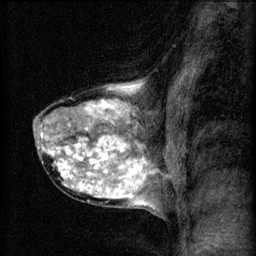
Breast MRI (dynamic contrast-enhanced), one sagittal slice. Position 36 of 60 along the scan axis. 3 images stored at this slice position (order not interpretable as contrast timing). 1.5 T. TE 4.2 ms, TR 8.2 ms. 2 mm slice thickness. 256 × 256 image matrix. Female patient, age 40 years.
Outlined on this slice (semi-automatic segmentation, software-assisted and operator-edited):
- analysis volume of interest (the breast-tissue region the enhancement analysis was run in; not a lesion): bounding box <33,80,167,211> (left, top, right, bottom; pixels)
- tumour enhancement mask (voxels above the 70 % enhancement threshold inside the analysis volume of interest): <42,86,154,205>